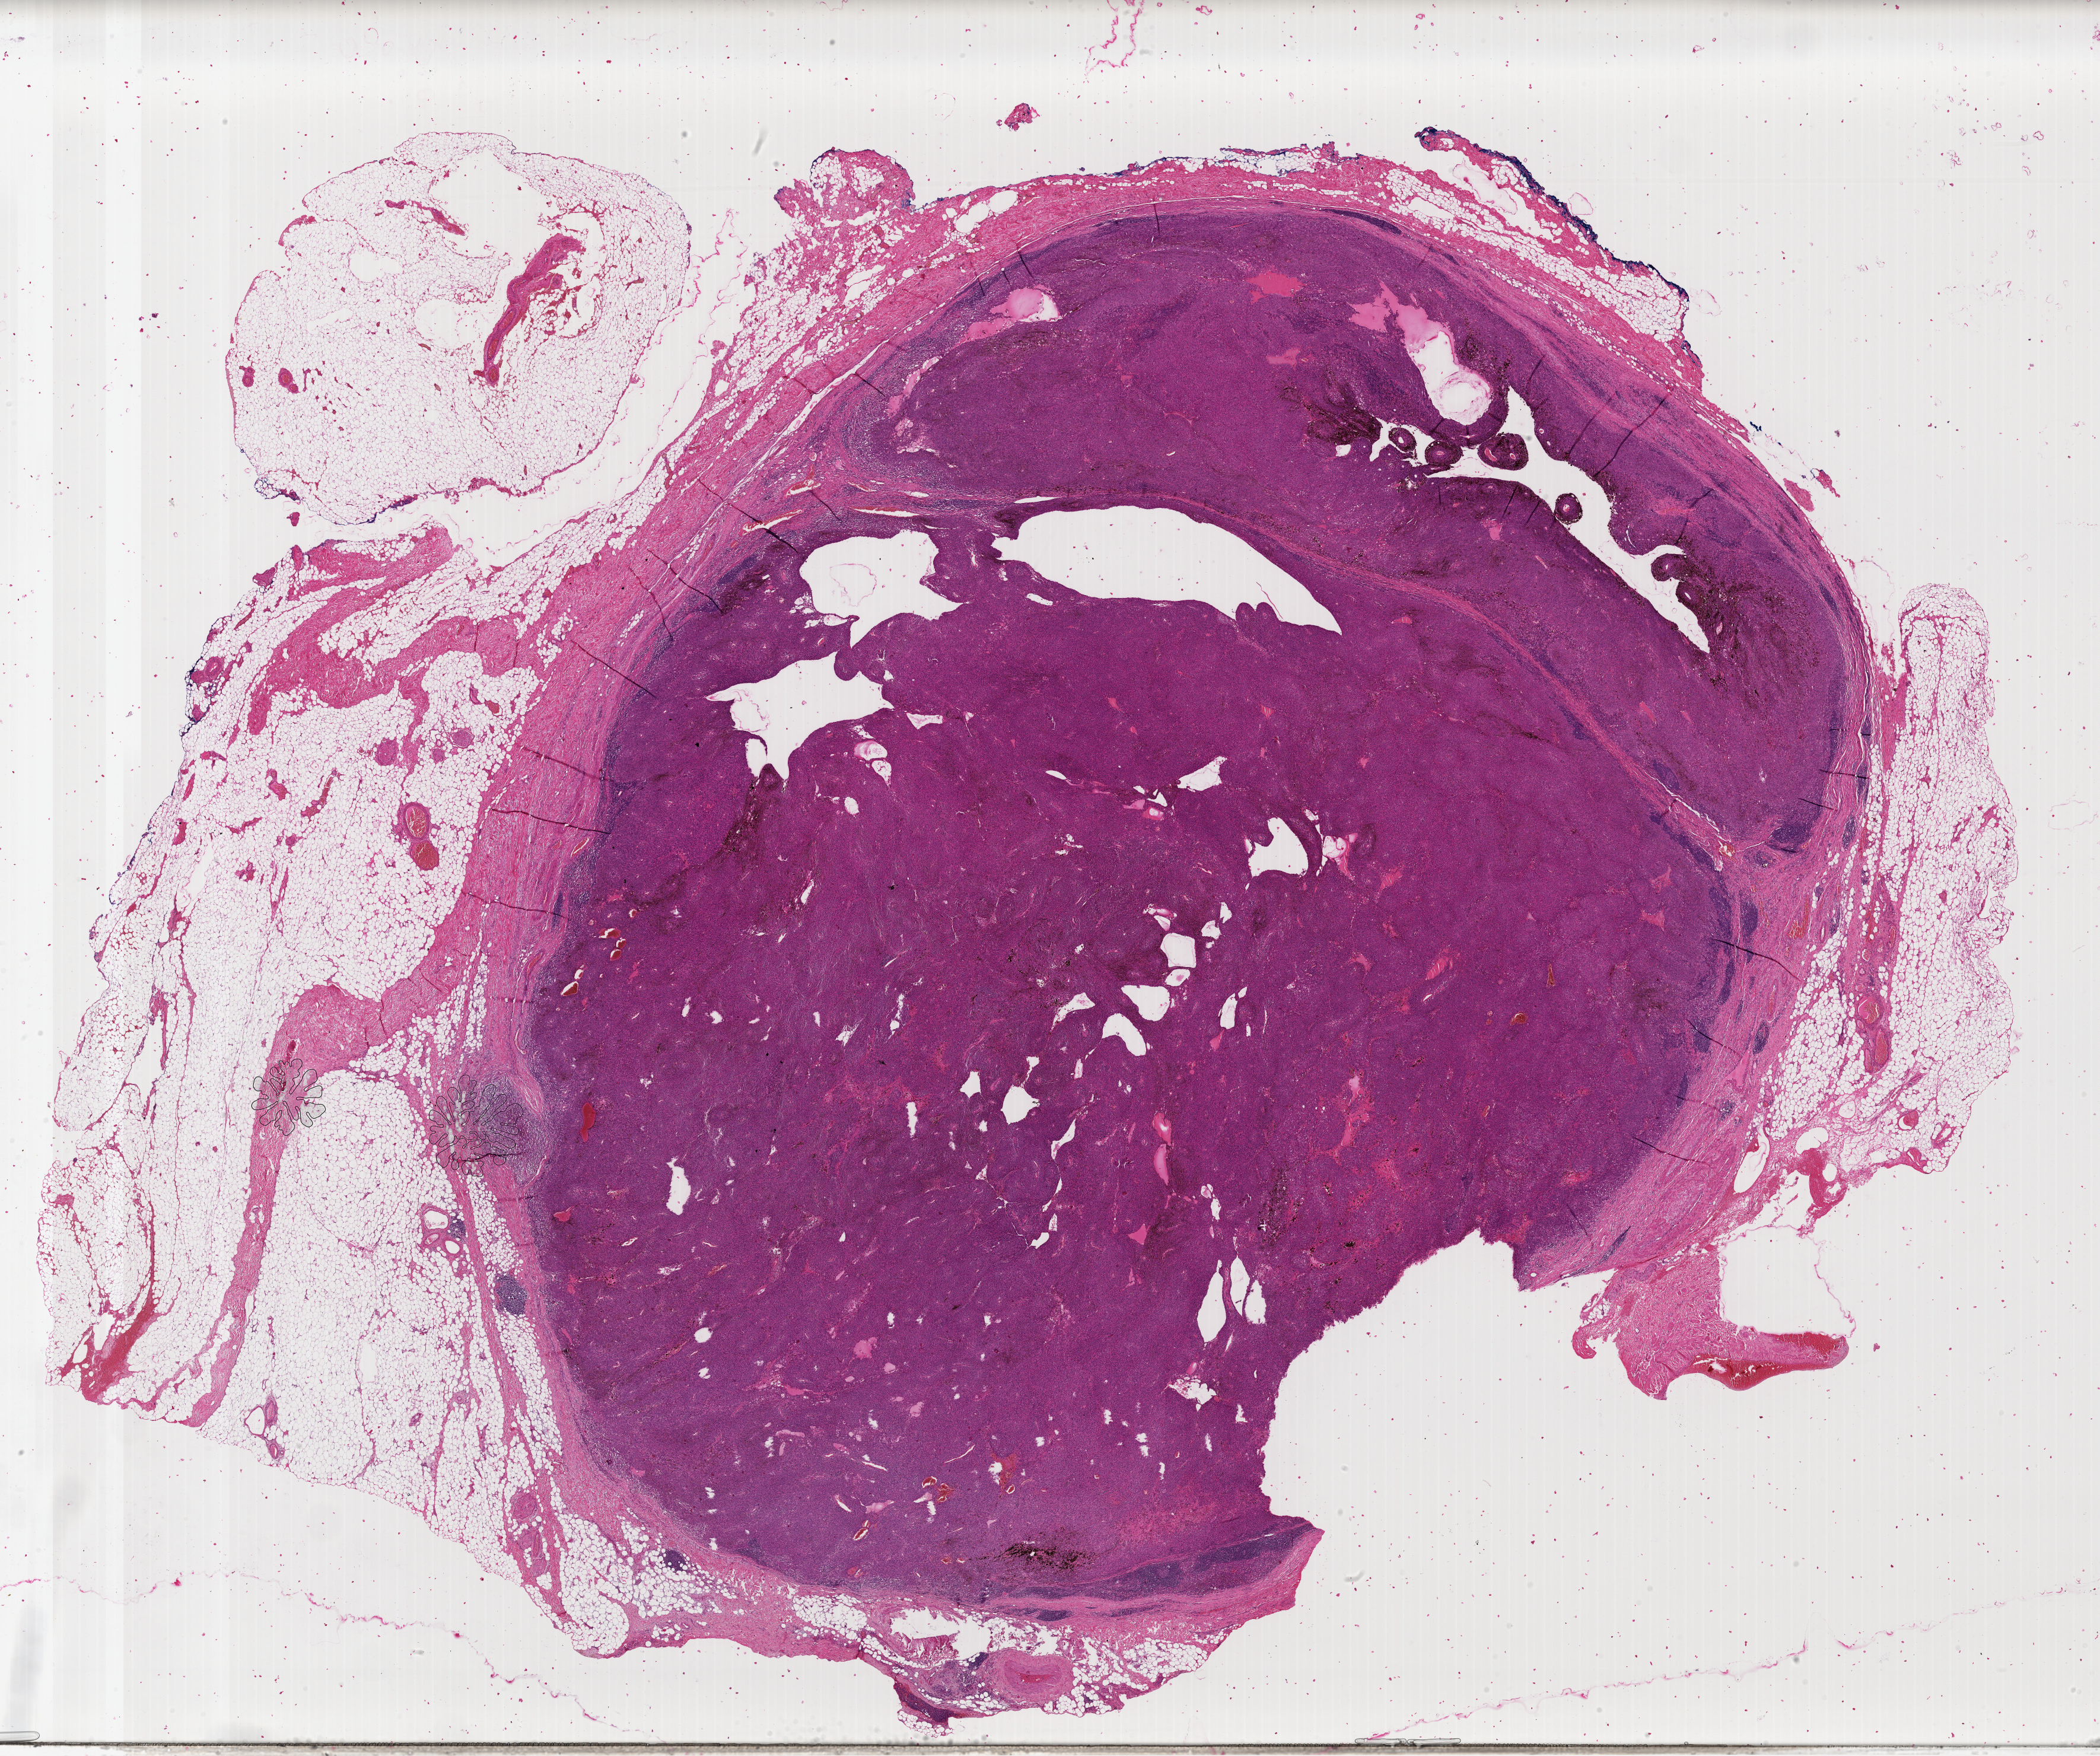
Whole-slide histology image, H&E — a low-resolution overview of the entire scanned area, about 28.0 x 23.4 mm; FFPE section; primary tumour sample from the skin. Patient: female, age at initial diagnosis 52 years.
Histologic diagnosis: Malignant melanoma, NOS.